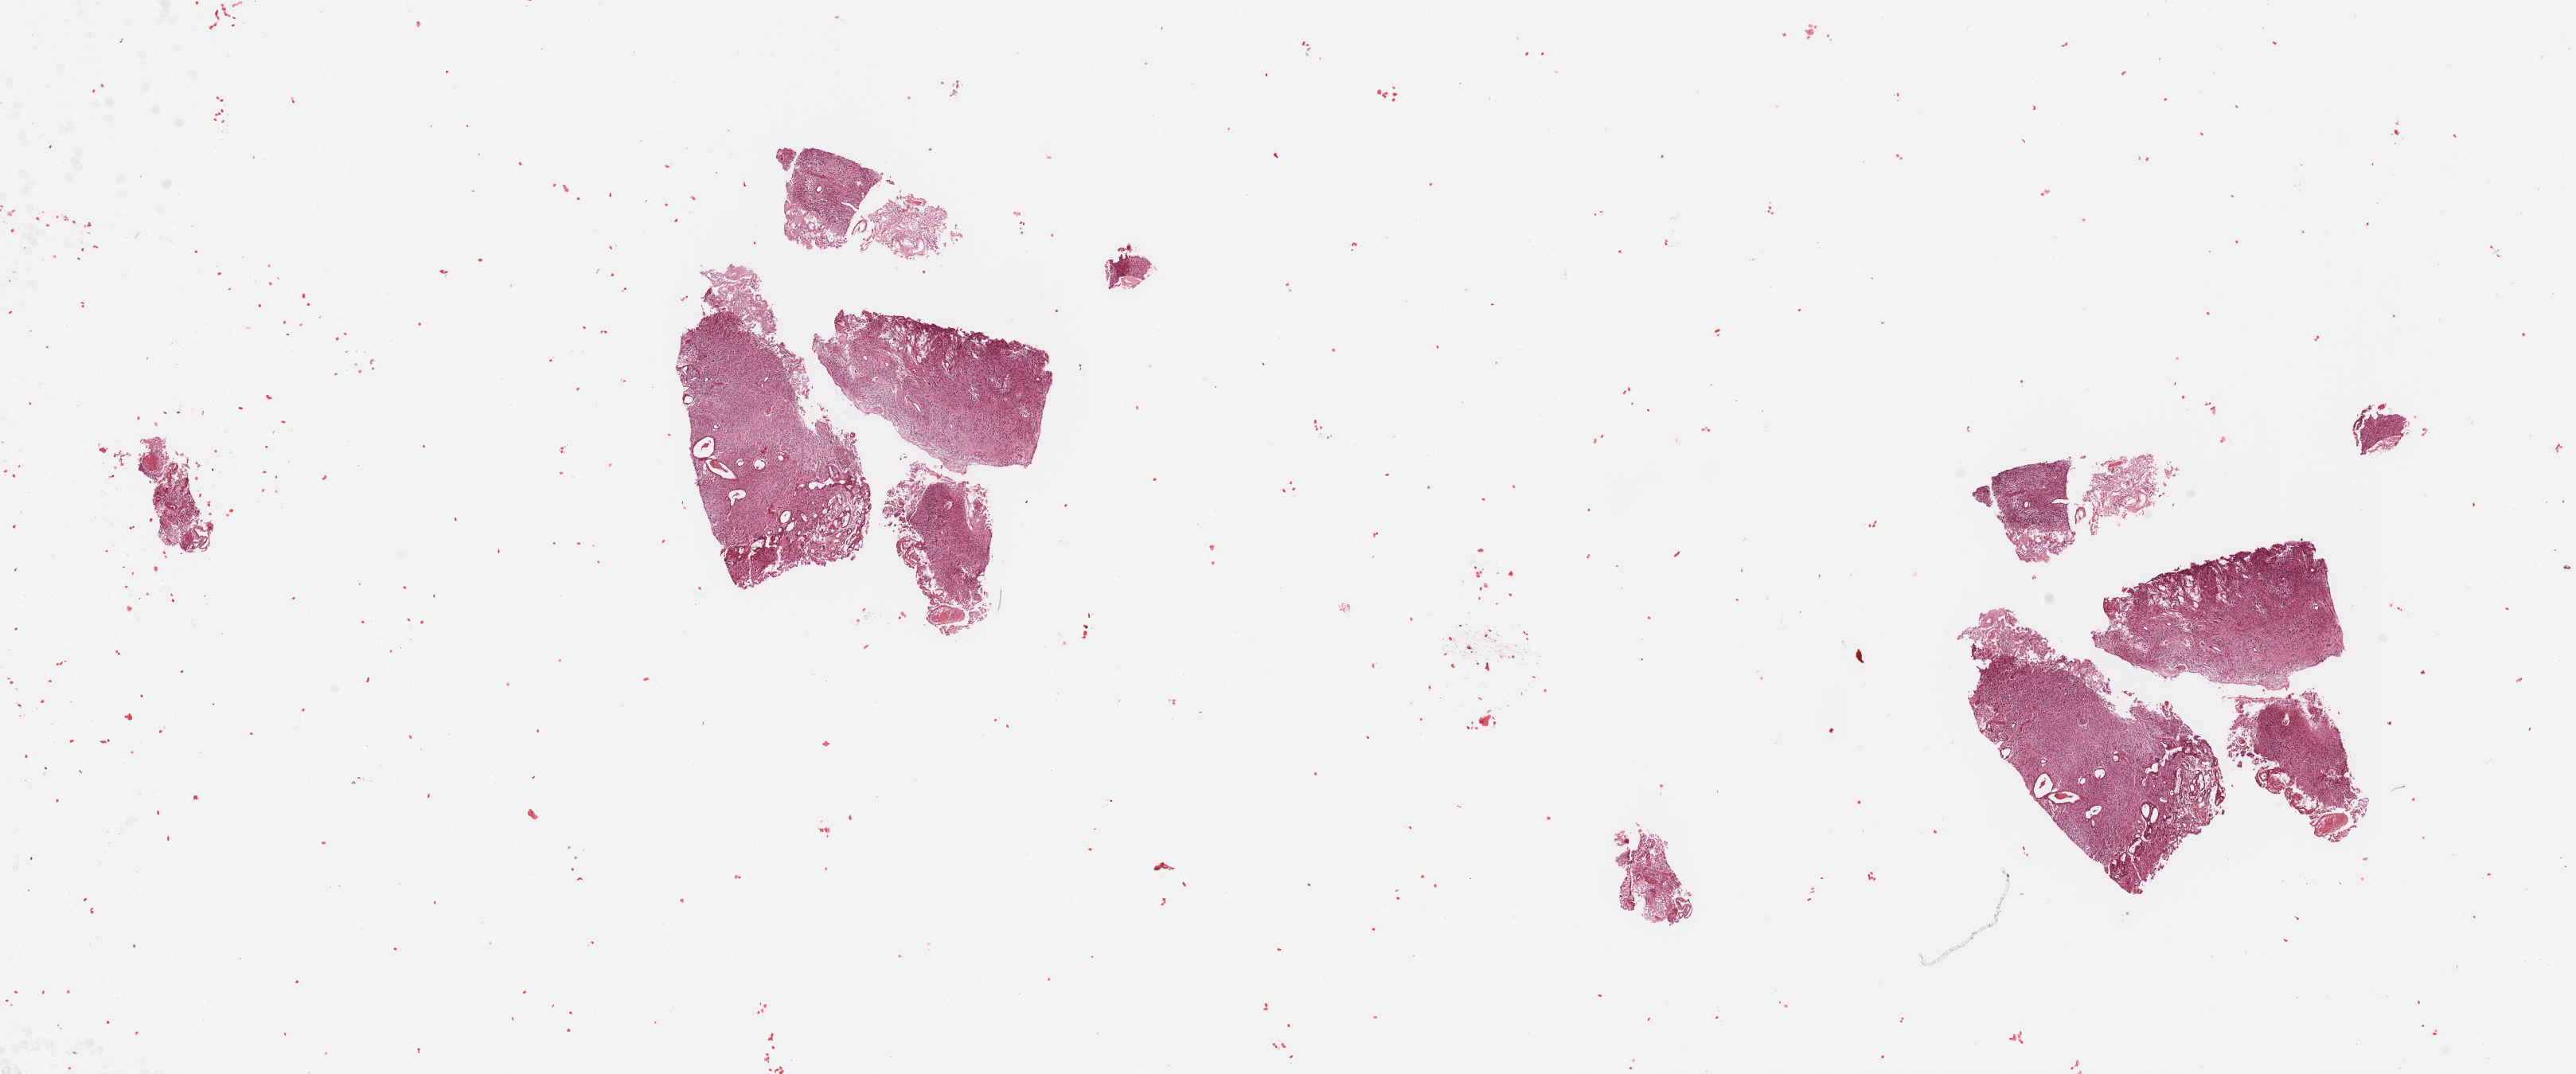
Hematoxylin and eosin (H&E) stained whole-slide image — whole scanned area (about 25.6 x 10.7 mm, acquisition: 20x scan) shown as a low-resolution overview; tumour tissue sample, brain. Female, 60 y/o.
Primary tumour site (as recorded): frontal lobe. Histologic diagnosis: Glioblastoma.